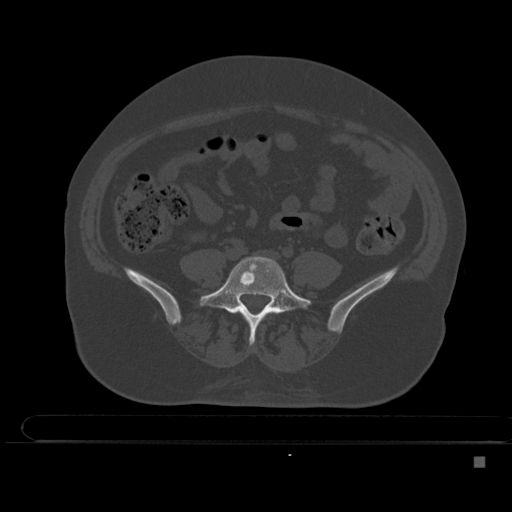
CT including the spine, one axial slice. Position 112 of 495 along the scan axis. Bone window (W 1800 / L 400 HU). 512 × 512 image matrix. Patient: female, 33 years. Case-level facts recorded for this patient, not image findings: primary cancer: breast.
Outlined on this slice (semi-automatic segmentation, software-assisted and operator-edited):
- L5 vertebra: box from (x=199, y=256) to (x=312, y=344) px